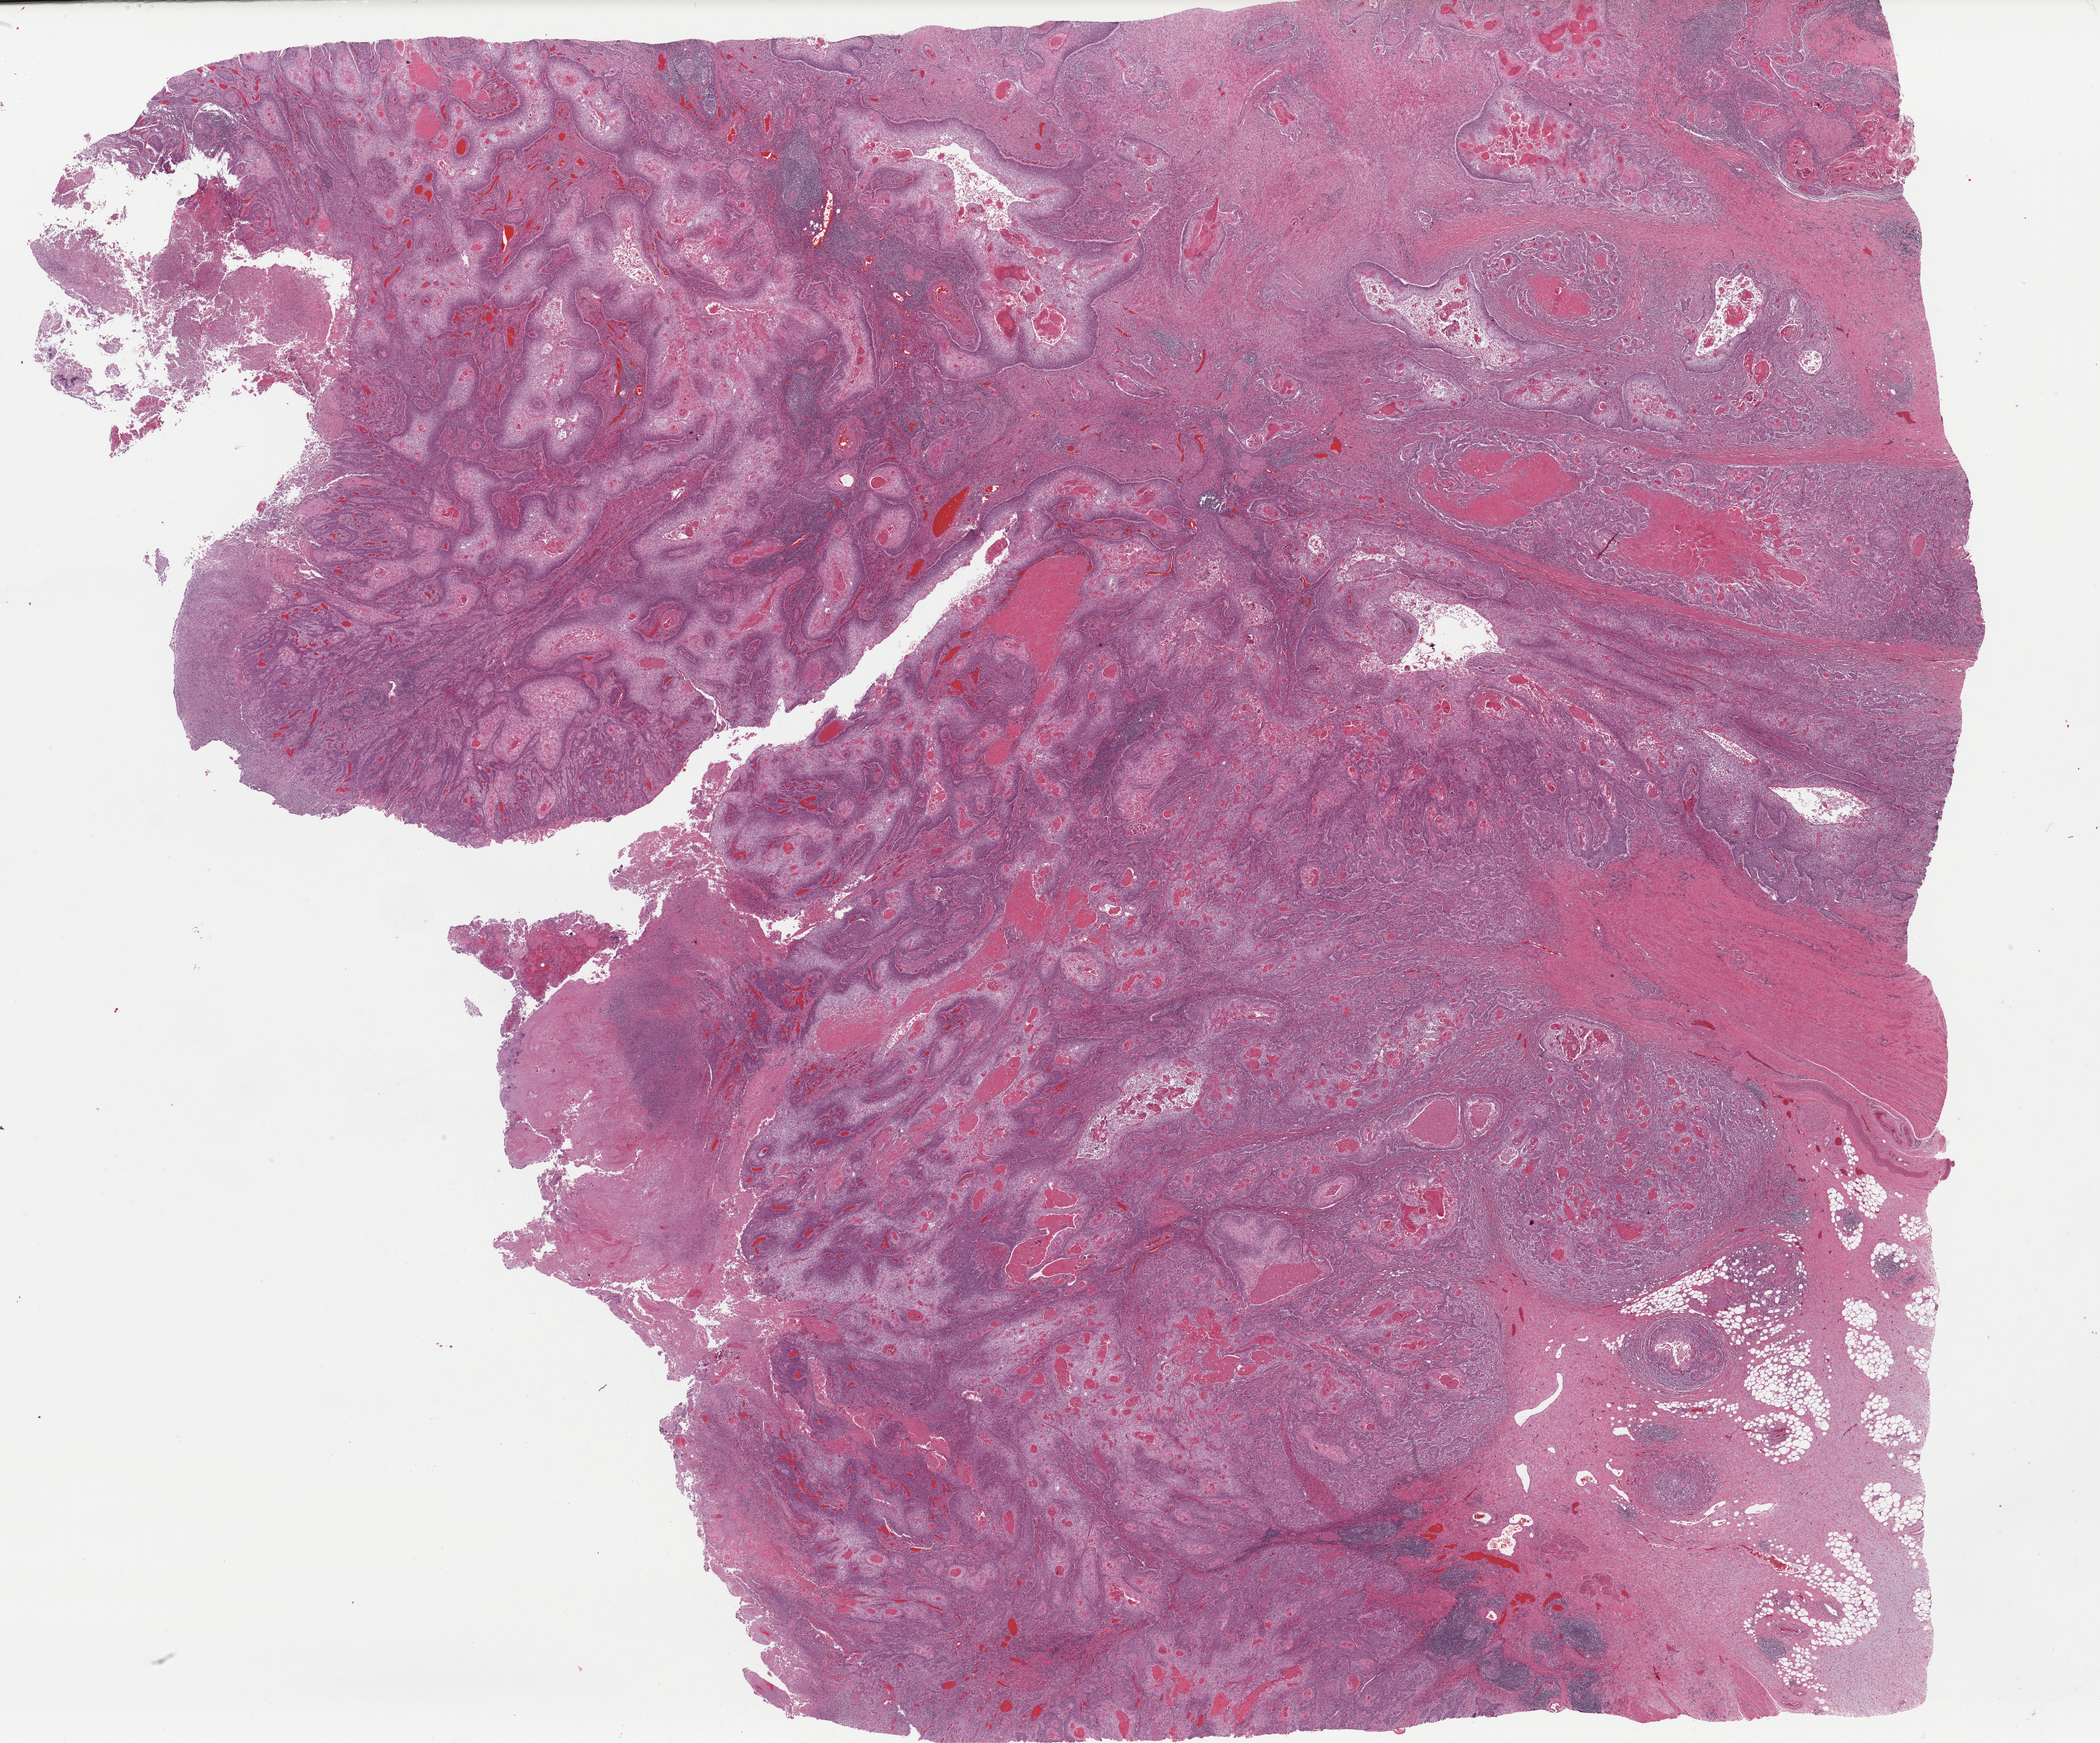
Digitized H&E tissue section (whole slide) — a low-resolution overview of the entire scanned area, about 28.0 x 23.2 mm (acquisition: 40x scan); formalin-fixed paraffin-embedded (FFPE) diagnostic section; bladder, primary tumour sample. Female patient; age at initial diagnosis 55 years. Histologic grade: high grade.
AJCC pathologic stage: III (7th edition). Pathologic diagnosis: Transitional cell carcinoma. Lymph nodes positive (case pathology): 0 of 27 examined.